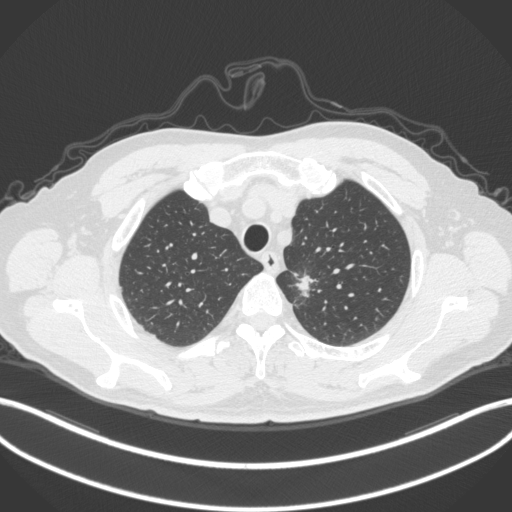
Chest CT, one axial slice. 120 kVp. Lung window (W 1500 / L -600 HU). 1 mm slice thickness. 512 × 512 image matrix. Male patient, age 64 years. Case-level facts recorded for this patient, not image findings: clinical TNM (as recorded): T1c N0 M0.
Outlined on this slice (rectangle marked by the reading radiologist):
- lung tumour (recorded histology: adenocarcinoma): bounding box (x1, y1, x2, y2) in pixels: (287, 271, 321, 307)